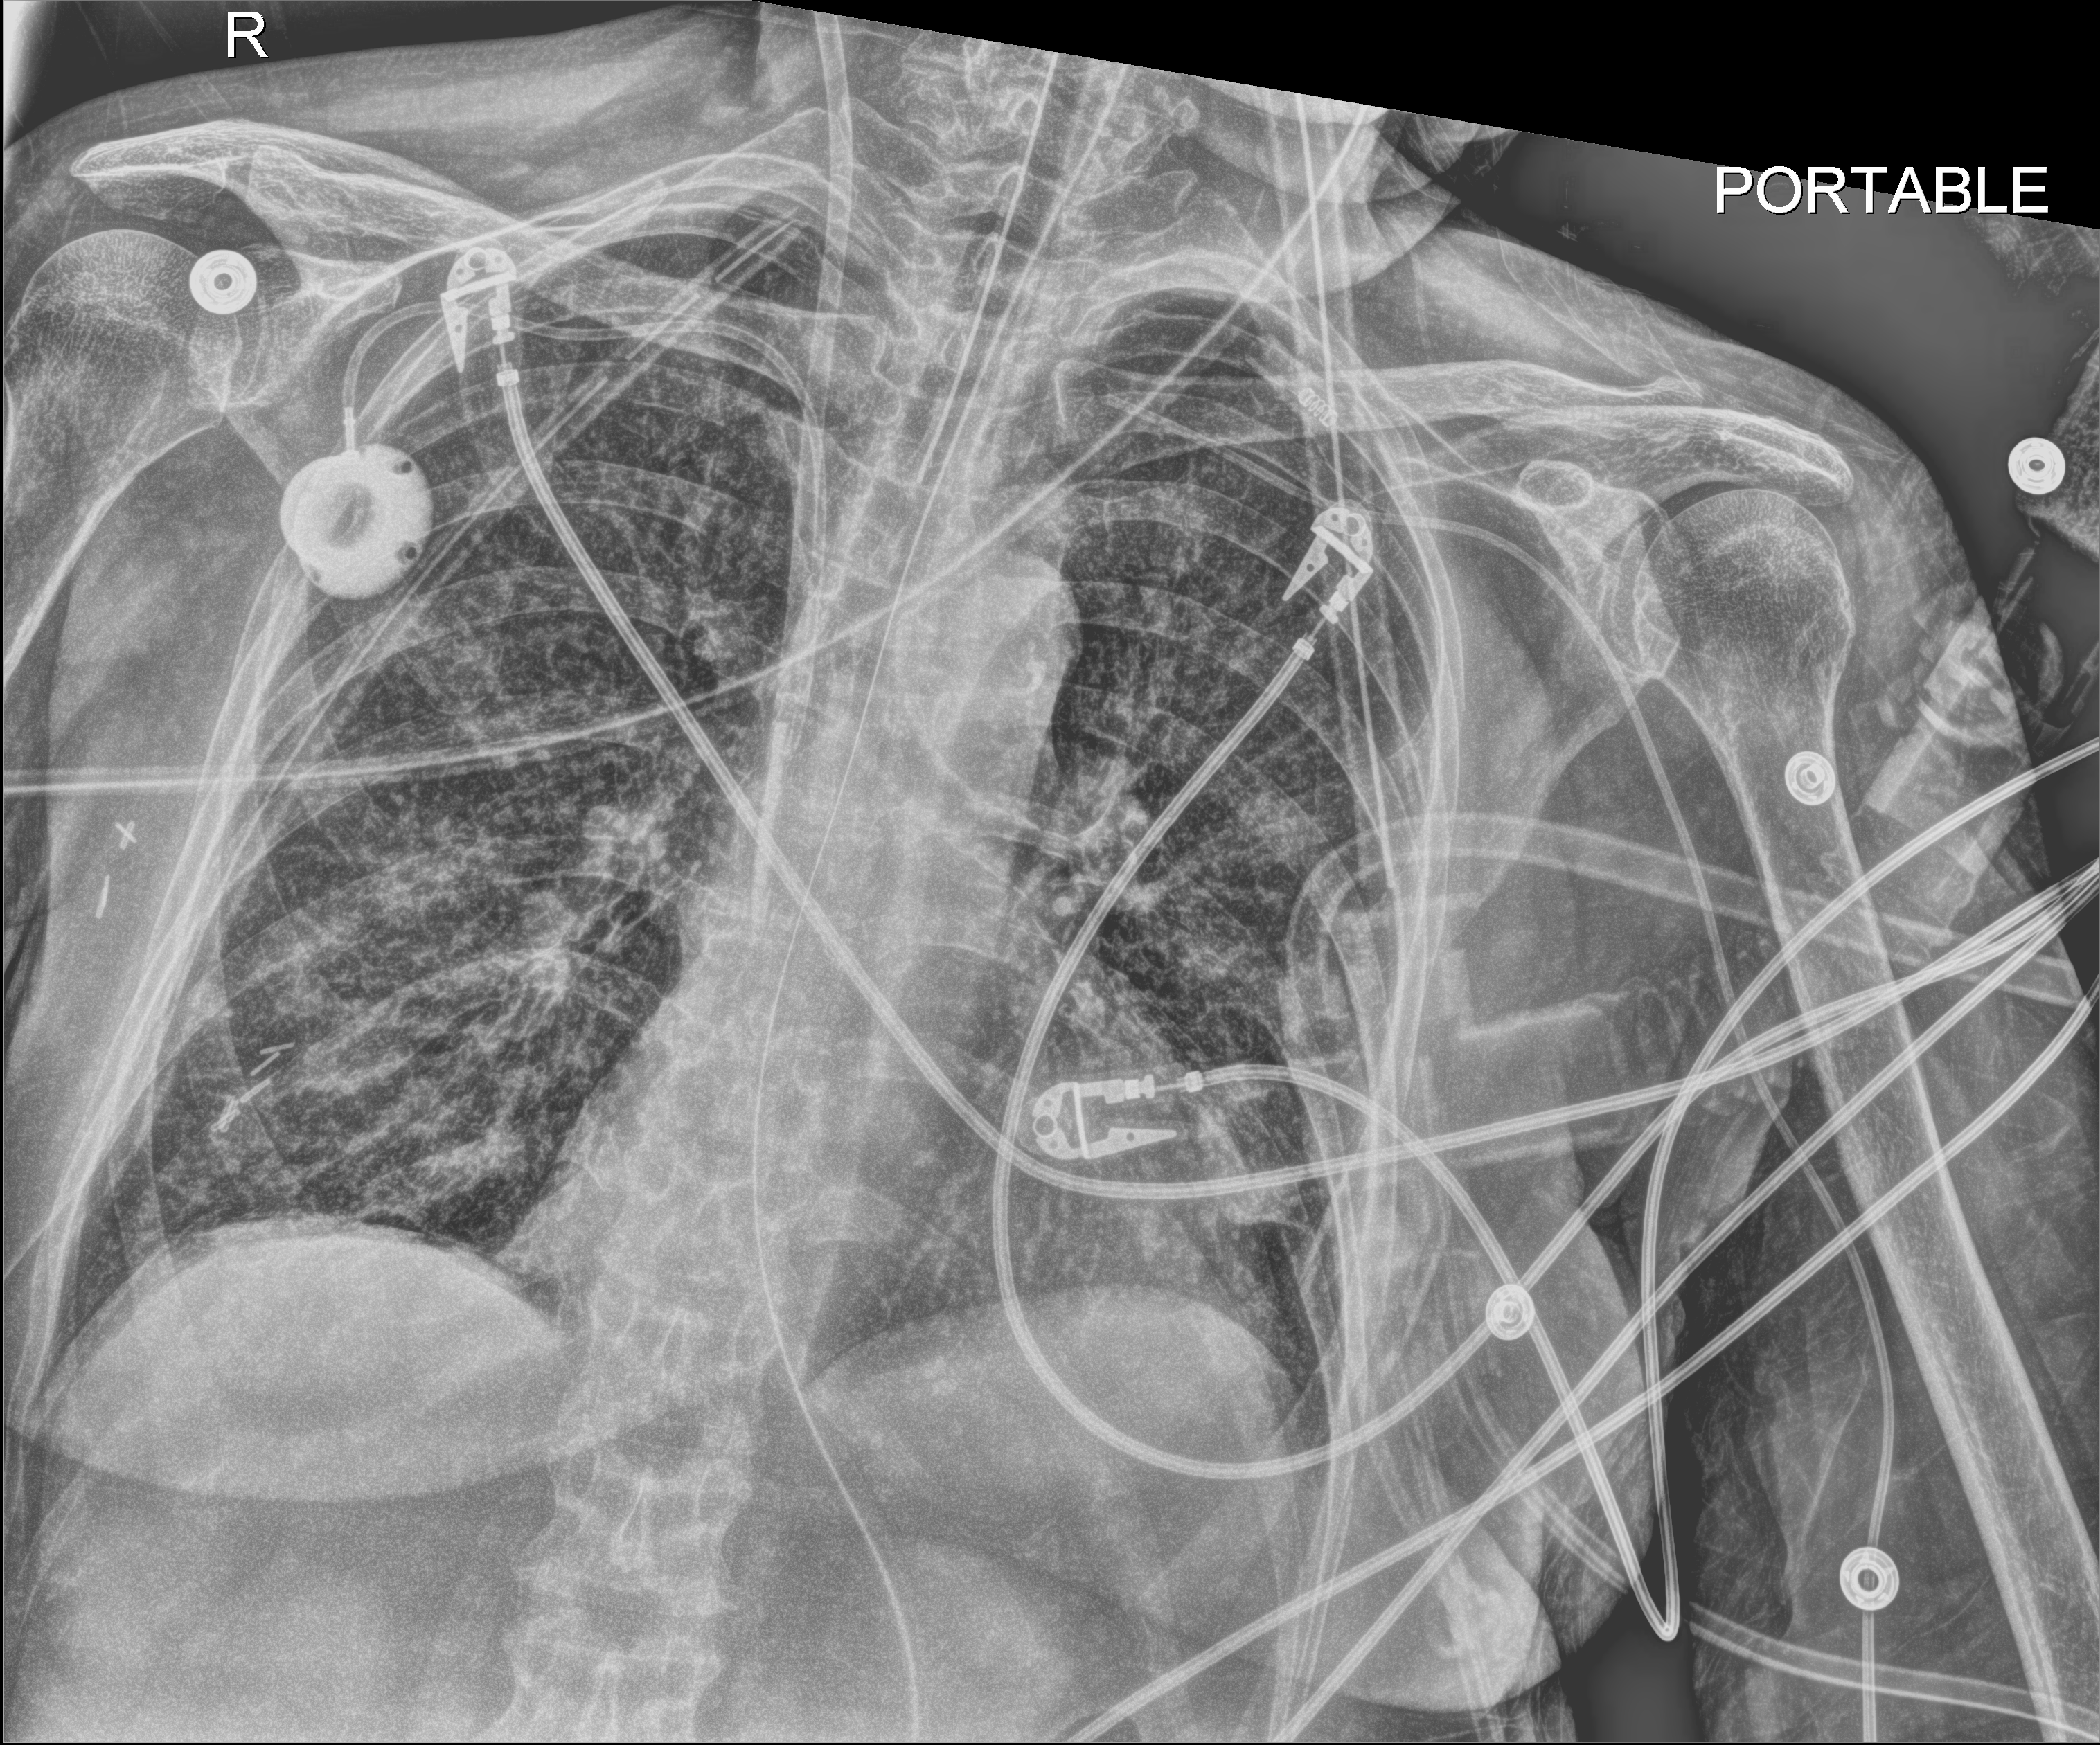
Portable chest radiograph; anteroposterior (AP) projection. Patient hospitalised with COVID-19; female, aged 60–74 years.
Hospital-stay facts (about this admission, not read from this image; timing relative to this image not recorded): admitted to intensive care during this hospital stay: yes; other chronic lung disease (admission record): no.